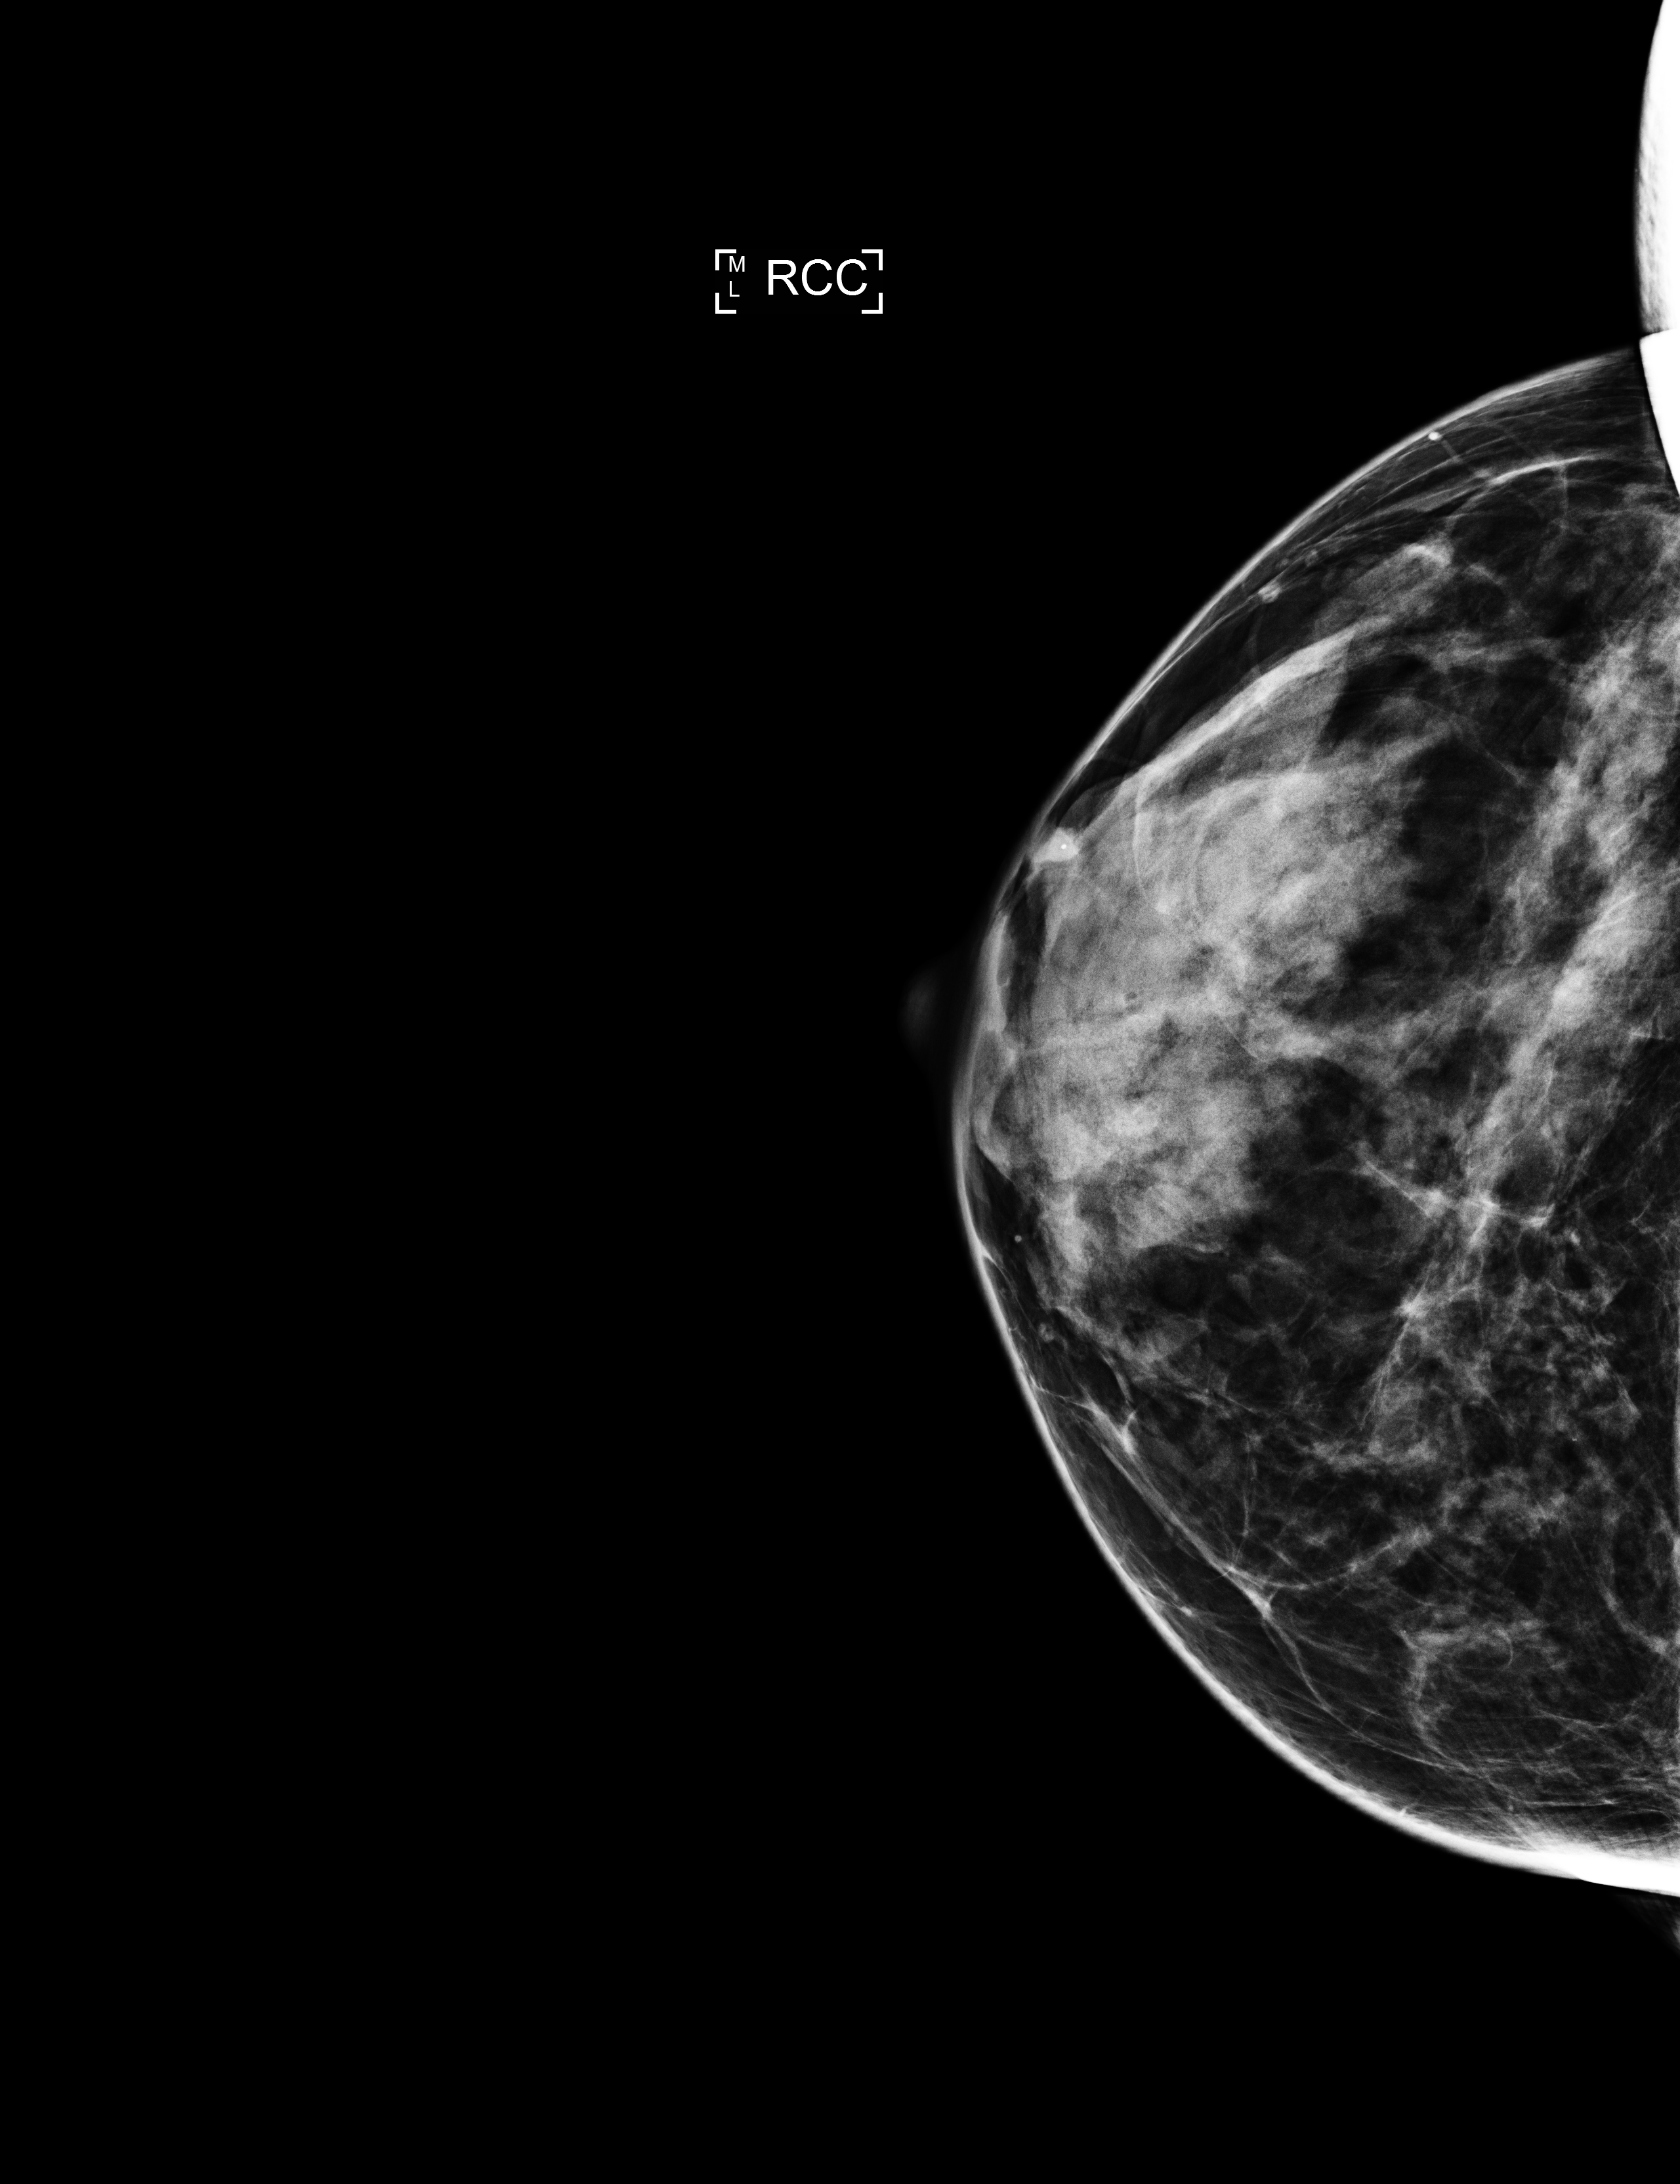
Screening examination. Patient: female, 53 years.
Image type: full-field digital mammogram. Breast: right. Projection: cranio-caudal projection.